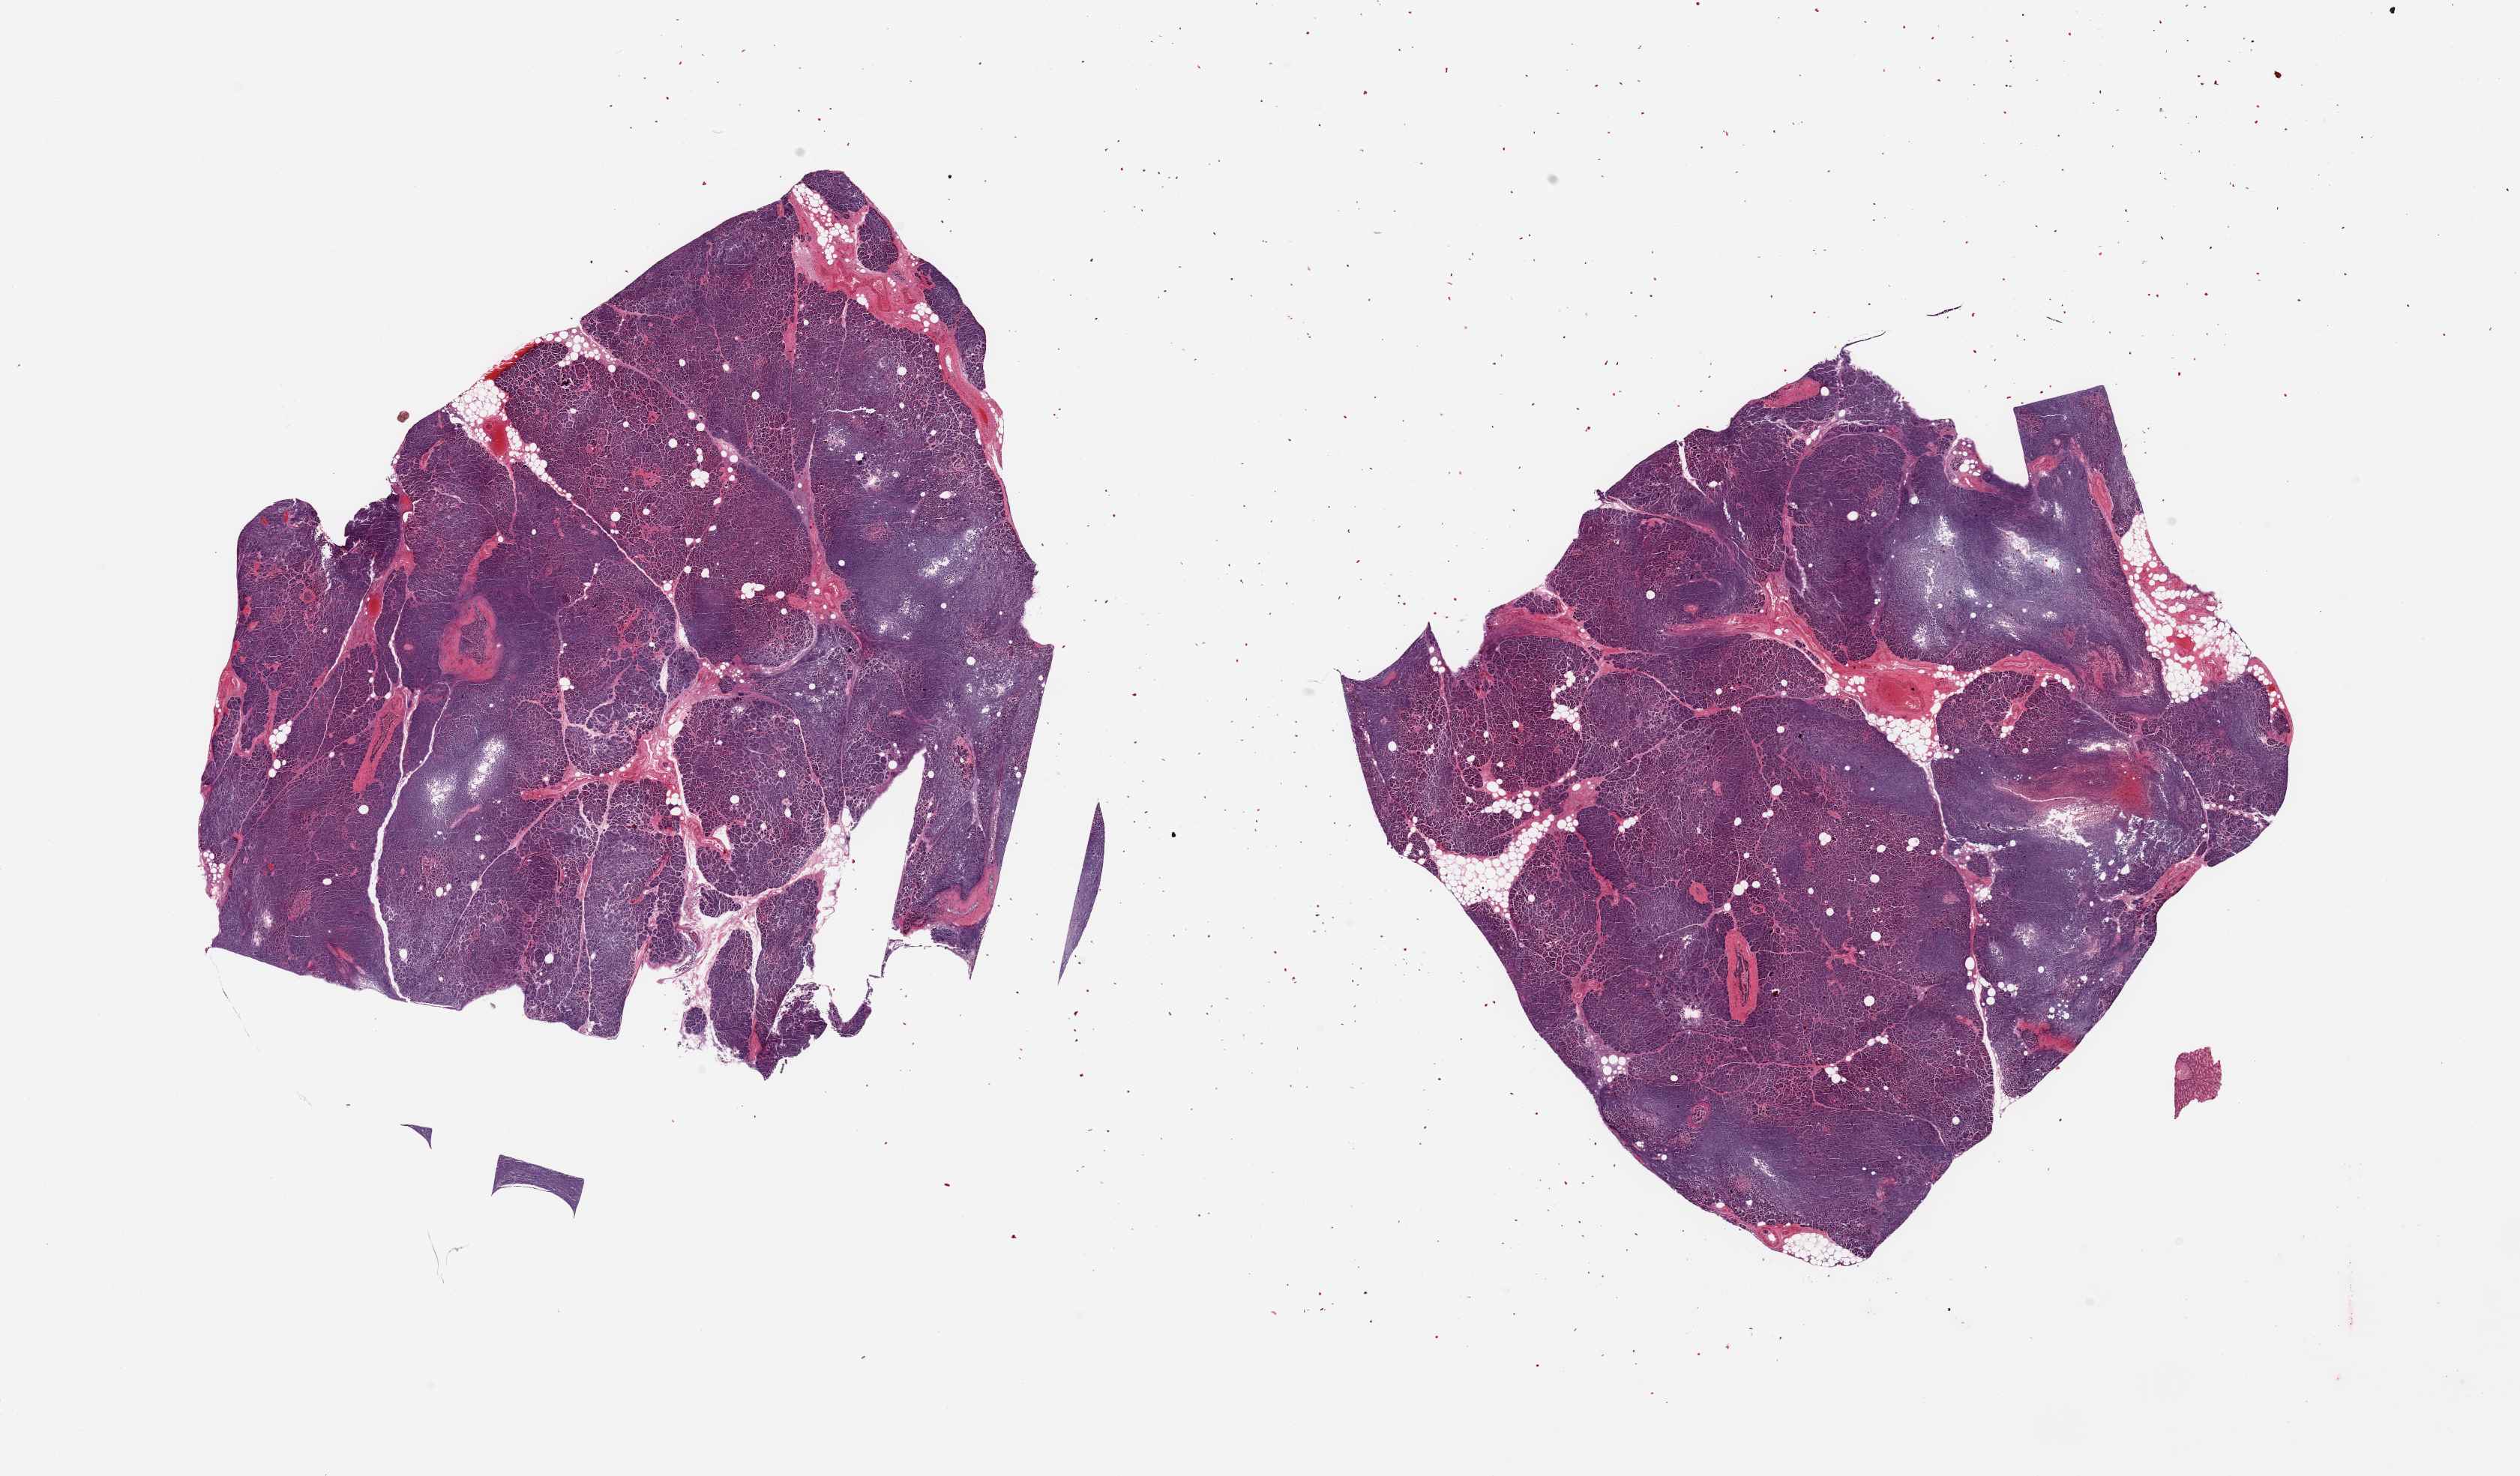
Digitized haematoxylin and eosin-stained section, brightfield — low-resolution overview of the scanned area, about 26.6 x 15.6 mm; PAXgene-fixed paraffin-embedded (PFPE) section; sampled site (target tissue): pancreas; tissue donor sample. Donor: male.
Reviewer comment on this tissue sample: 2 pieces; small component of fat, mild fibrosis, moderate to severe autolysis.